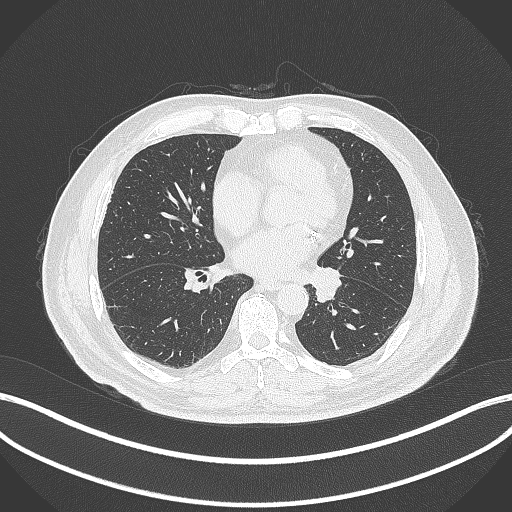
Chest CT, one axial slice. Slice 123 of 312 in the series (ordered by position). Reconstruction kernel B70f. 120 kVp. Lung window (W 1500 / L -600 HU). 1 mm slice thickness. 512 × 512 image matrix, field of view 400 × 400 mm. Male patient, age 71 years. Case-level facts recorded for this patient, not image findings: clinical TNM (as recorded): T1b N0 M0.
Outlined on this slice (rectangle marked by the reading radiologist):
- lung tumour (recorded histology: squamous cell carcinoma): bounding box (x1, y1, x2, y2) in pixels: (307, 264, 344, 304)